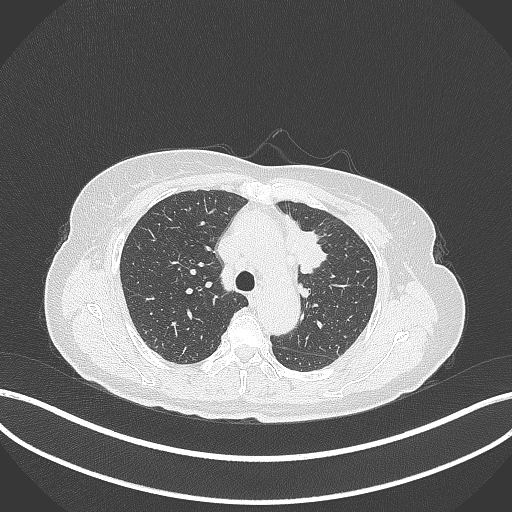
Chest CT, one axial slice; slice 238 of 369 in the series (ordered by position); reconstruction kernel B70f; lung window (W 1500 / L -600 HU); 1 mm slice thickness; 512 × 512 image matrix. Female patient, age 65 years. From the clinical record (not read from this slice): clinical TNM (as recorded): T2a N0 M0; histopathological grade: G2-3.
Structures marked on this image (bounding box drawn by a radiologist):
- lung tumour (recorded histology: adenocarcinoma): box from (x=282, y=214) to (x=328, y=274) px